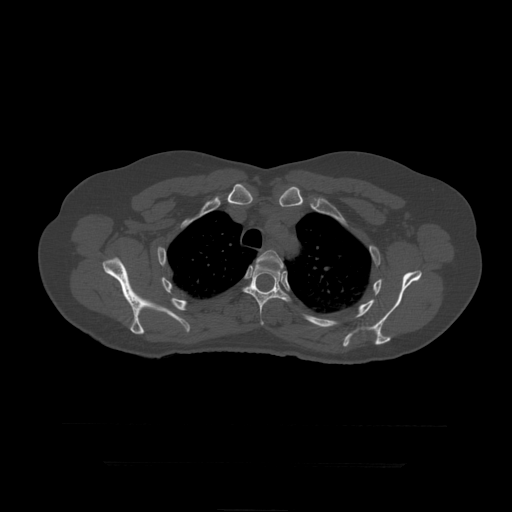
CT including the spine, one axial slice; position 338 of 399 along the scan axis; 120 kVp; bone window (W 1800 / L 400 HU); 1.25 mm slice thickness; 512 × 512 image matrix. Patient age 41 years. From the clinical record (not read from this slice): primary cancer: breast.
Outlined on this slice (semi-automatically segmented with operator editing):
- T4 vertebra: box from (x=255, y=250) to (x=284, y=273) px
- T5 vertebra: (x=243, y=265)–(x=292, y=325)